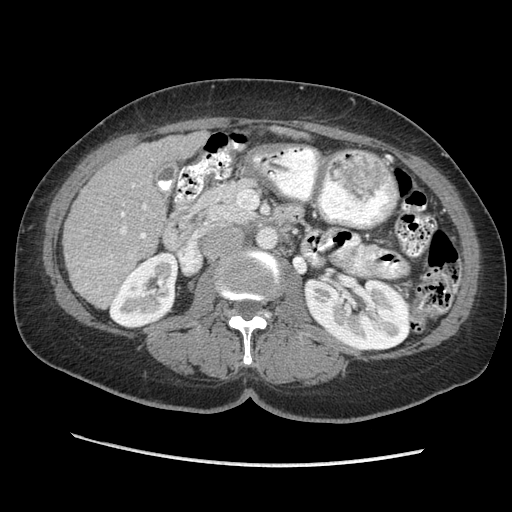
Contrast-enhanced abdominal CT (liver protocol), one axial slice; slice 108 of 170 in the series (ordered by position); reconstruction kernel STANDARD; soft-tissue window (W 400 / L 40 HU); 2.5 mm slice thickness; 512 × 512 image matrix, field of view 360 × 360 mm. From the clinical record (not read from this slice): diagnosis: hepatocellular carcinoma (patient treated with transarterial chemoembolisation; whether this scan precedes or follows treatment is not stated here); TNM stage (as recorded): Stage-II.
Outlined on this slice (semi-automatically segmented with operator editing):
- liver parenchyma outside the tumour (the mass and vessels are separate outlines, so this box may not span the whole liver): bounding box [x1, y1, x2, y2] px = [62, 132, 208, 308]
- liver vessels: [111, 184, 147, 257]